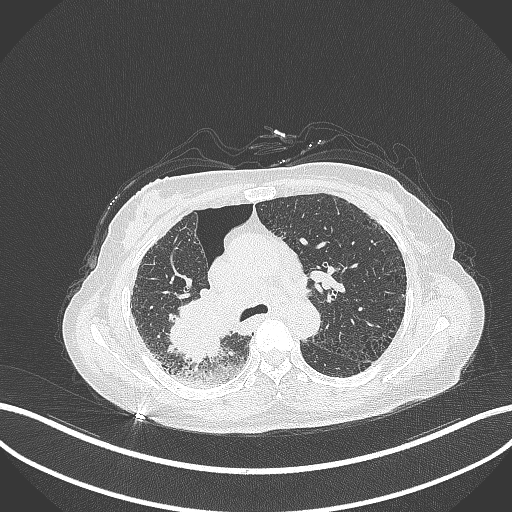
Chest CT, one axial slice; slice 226 of 408 in the series (ordered by position); reconstruction kernel B70f; 120 kVp; lung window (W 1500 / L -600 HU); 512 × 512 image matrix, field of view 400 × 400 mm. Female patient, age 64 years. From the clinical record (not read from this slice): clinical TNM (as recorded): T3 N3 M0.
Outlined on this slice (rectangle marked by the reading radiologist):
- lung tumour (recorded histology: squamous cell carcinoma): bounding box (x1, y1, x2, y2) in pixels: (161, 287, 236, 367)